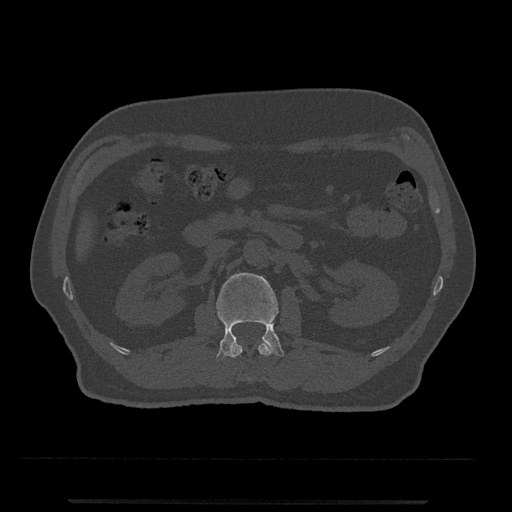
CT including the spine, one axial slice; slice 289 of 797 in the series (ordered by position); 120 kVp; bone window (W 1800 / L 400 HU); 0.5 mm slice thickness; 512 × 512 image matrix, field of view 419 × 419 mm. Patient: male, 63 years. From the clinical record (not read from this slice): primary cancer: prostate.
Outlined on this slice (semi-automatic segmentation, software-assisted and operator-edited):
- L1 vertebra: bounding box <230,342,273,380> (left, top, right, bottom; pixels)
- L2 vertebra: <216,272,284,360>